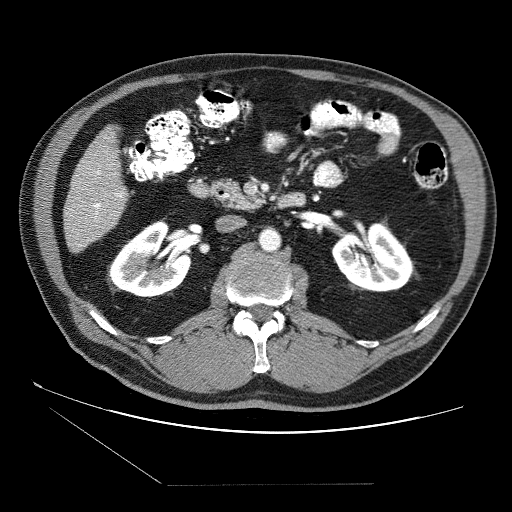
Contrast-enhanced abdominal CT (liver protocol), one axial slice; slice 16 of 87 in the series (ordered by position); reconstruction kernel STANDARD; soft-tissue window (W 400 / L 40 HU); 512 × 512 image matrix, field of view 400 × 400 mm. Case-level facts recorded for this patient, not image findings: diagnosis: hepatocellular carcinoma (patient treated with transarterial chemoembolisation; whether this scan precedes or follows treatment is not stated here); TNM stage (as recorded): Stage-II; Child-Pugh class: B; tumour differentiation: no biopsy; tumour nodularity: multinodular.
Outlined on this slice (semi-automatic segmentation, software-assisted and operator-edited):
- liver parenchyma outside the tumour (the mass and vessels are separate outlines, so this box may not span the whole liver): box from (x=64, y=126) to (x=128, y=252) px
- liver vessels: (x=71, y=164)–(x=124, y=246)